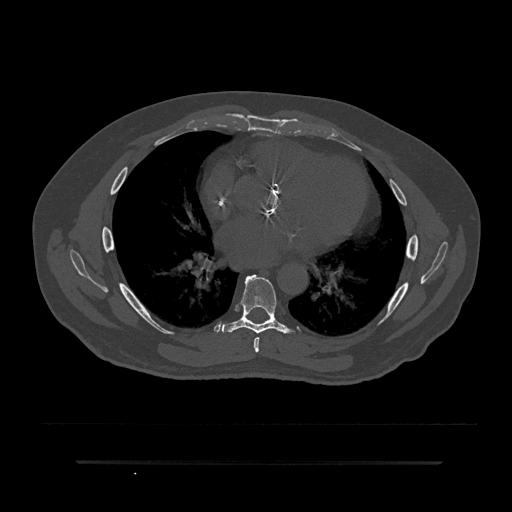
CT including the spine, one axial slice; position 484 of 797 along the scan axis; reconstruction kernel Br40s/3; bone window (W 1800 / L 400 HU); 0.5 mm slice thickness; 512 × 512 image matrix. Patient: male, 59 years. From the clinical record (not read from this slice): primary cancer: bile ducts; vertebrae with lytic lesions (as recorded): T10.
Annotated regions visible in this slice (semi-automatically segmented with operator editing):
- T6 vertebra: bounding box <253,337,260,353> (left, top, right, bottom; pixels)
- T7 vertebra: <222,274,294,334>